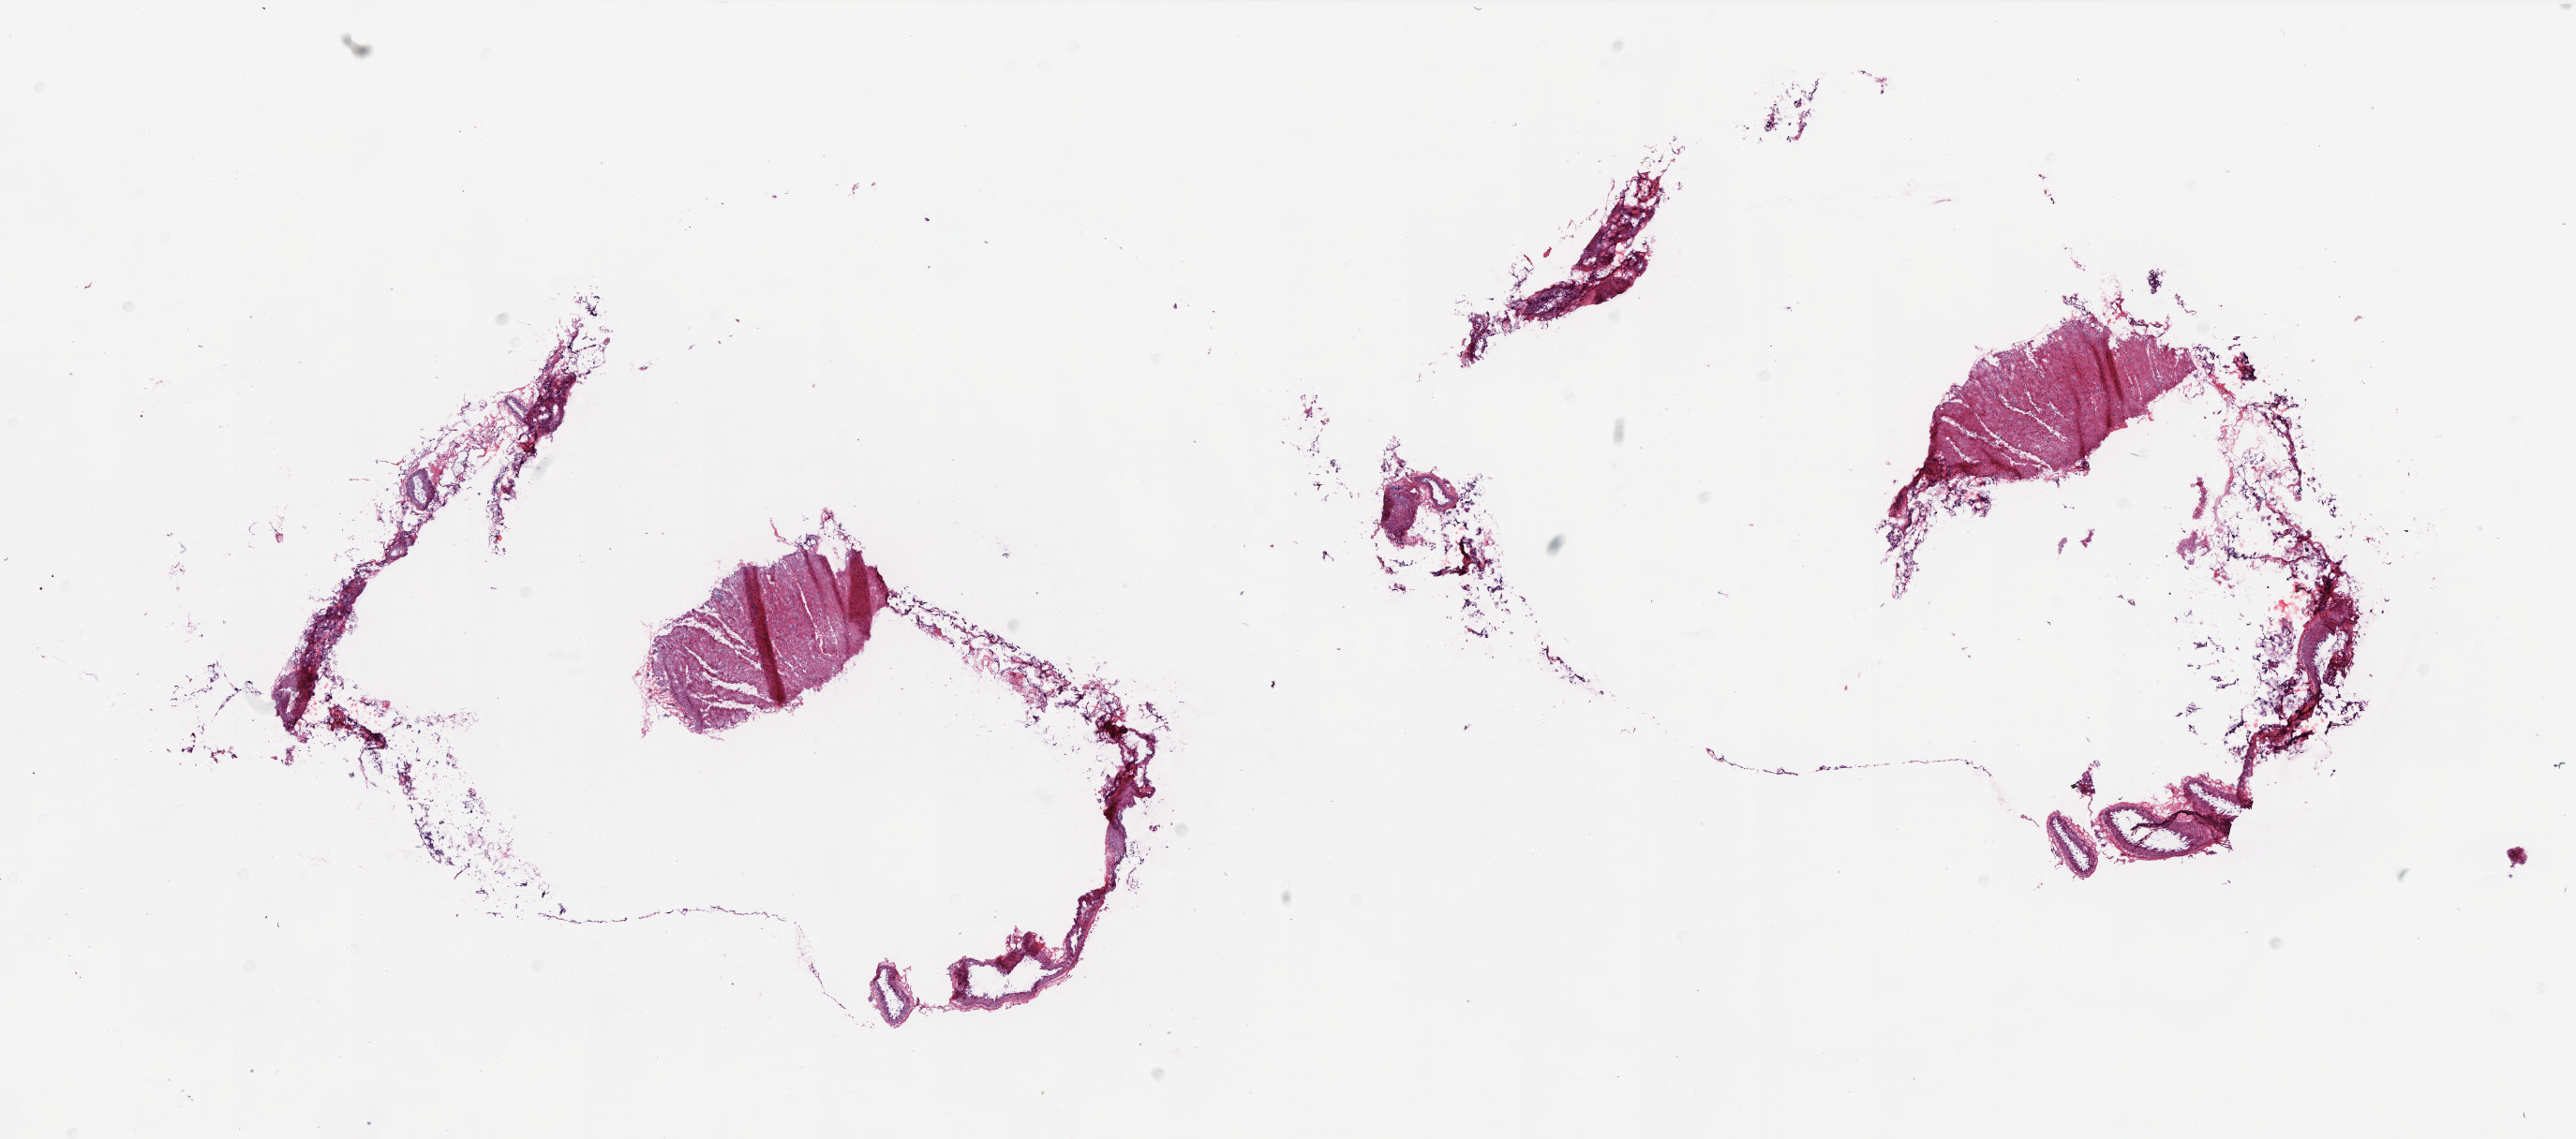
Whole-slide histology image, Hematoxylin and eosin (H&E) stained, shown as a low-resolution overview of the whole scanned area (about 22.0 x 9.7 mm, slide scanned at 20x). Frozen section. Solid tissue normal (non-tumour tissue) sample from the colon. Female, age 47 years at initial diagnosis. Slide review estimates, as recorded: tumour cells 0%, normal cells 100%. Inflammatory infiltration, as recorded: lymphocyte infiltration 4%, monocyte infiltration 1%, neutrophil infiltration 0%.
• this section: solid tissue normal (non-tumour) sample from the same patient
• patient diagnosis: Adenocarcinoma, NOS (sigmoid colon)